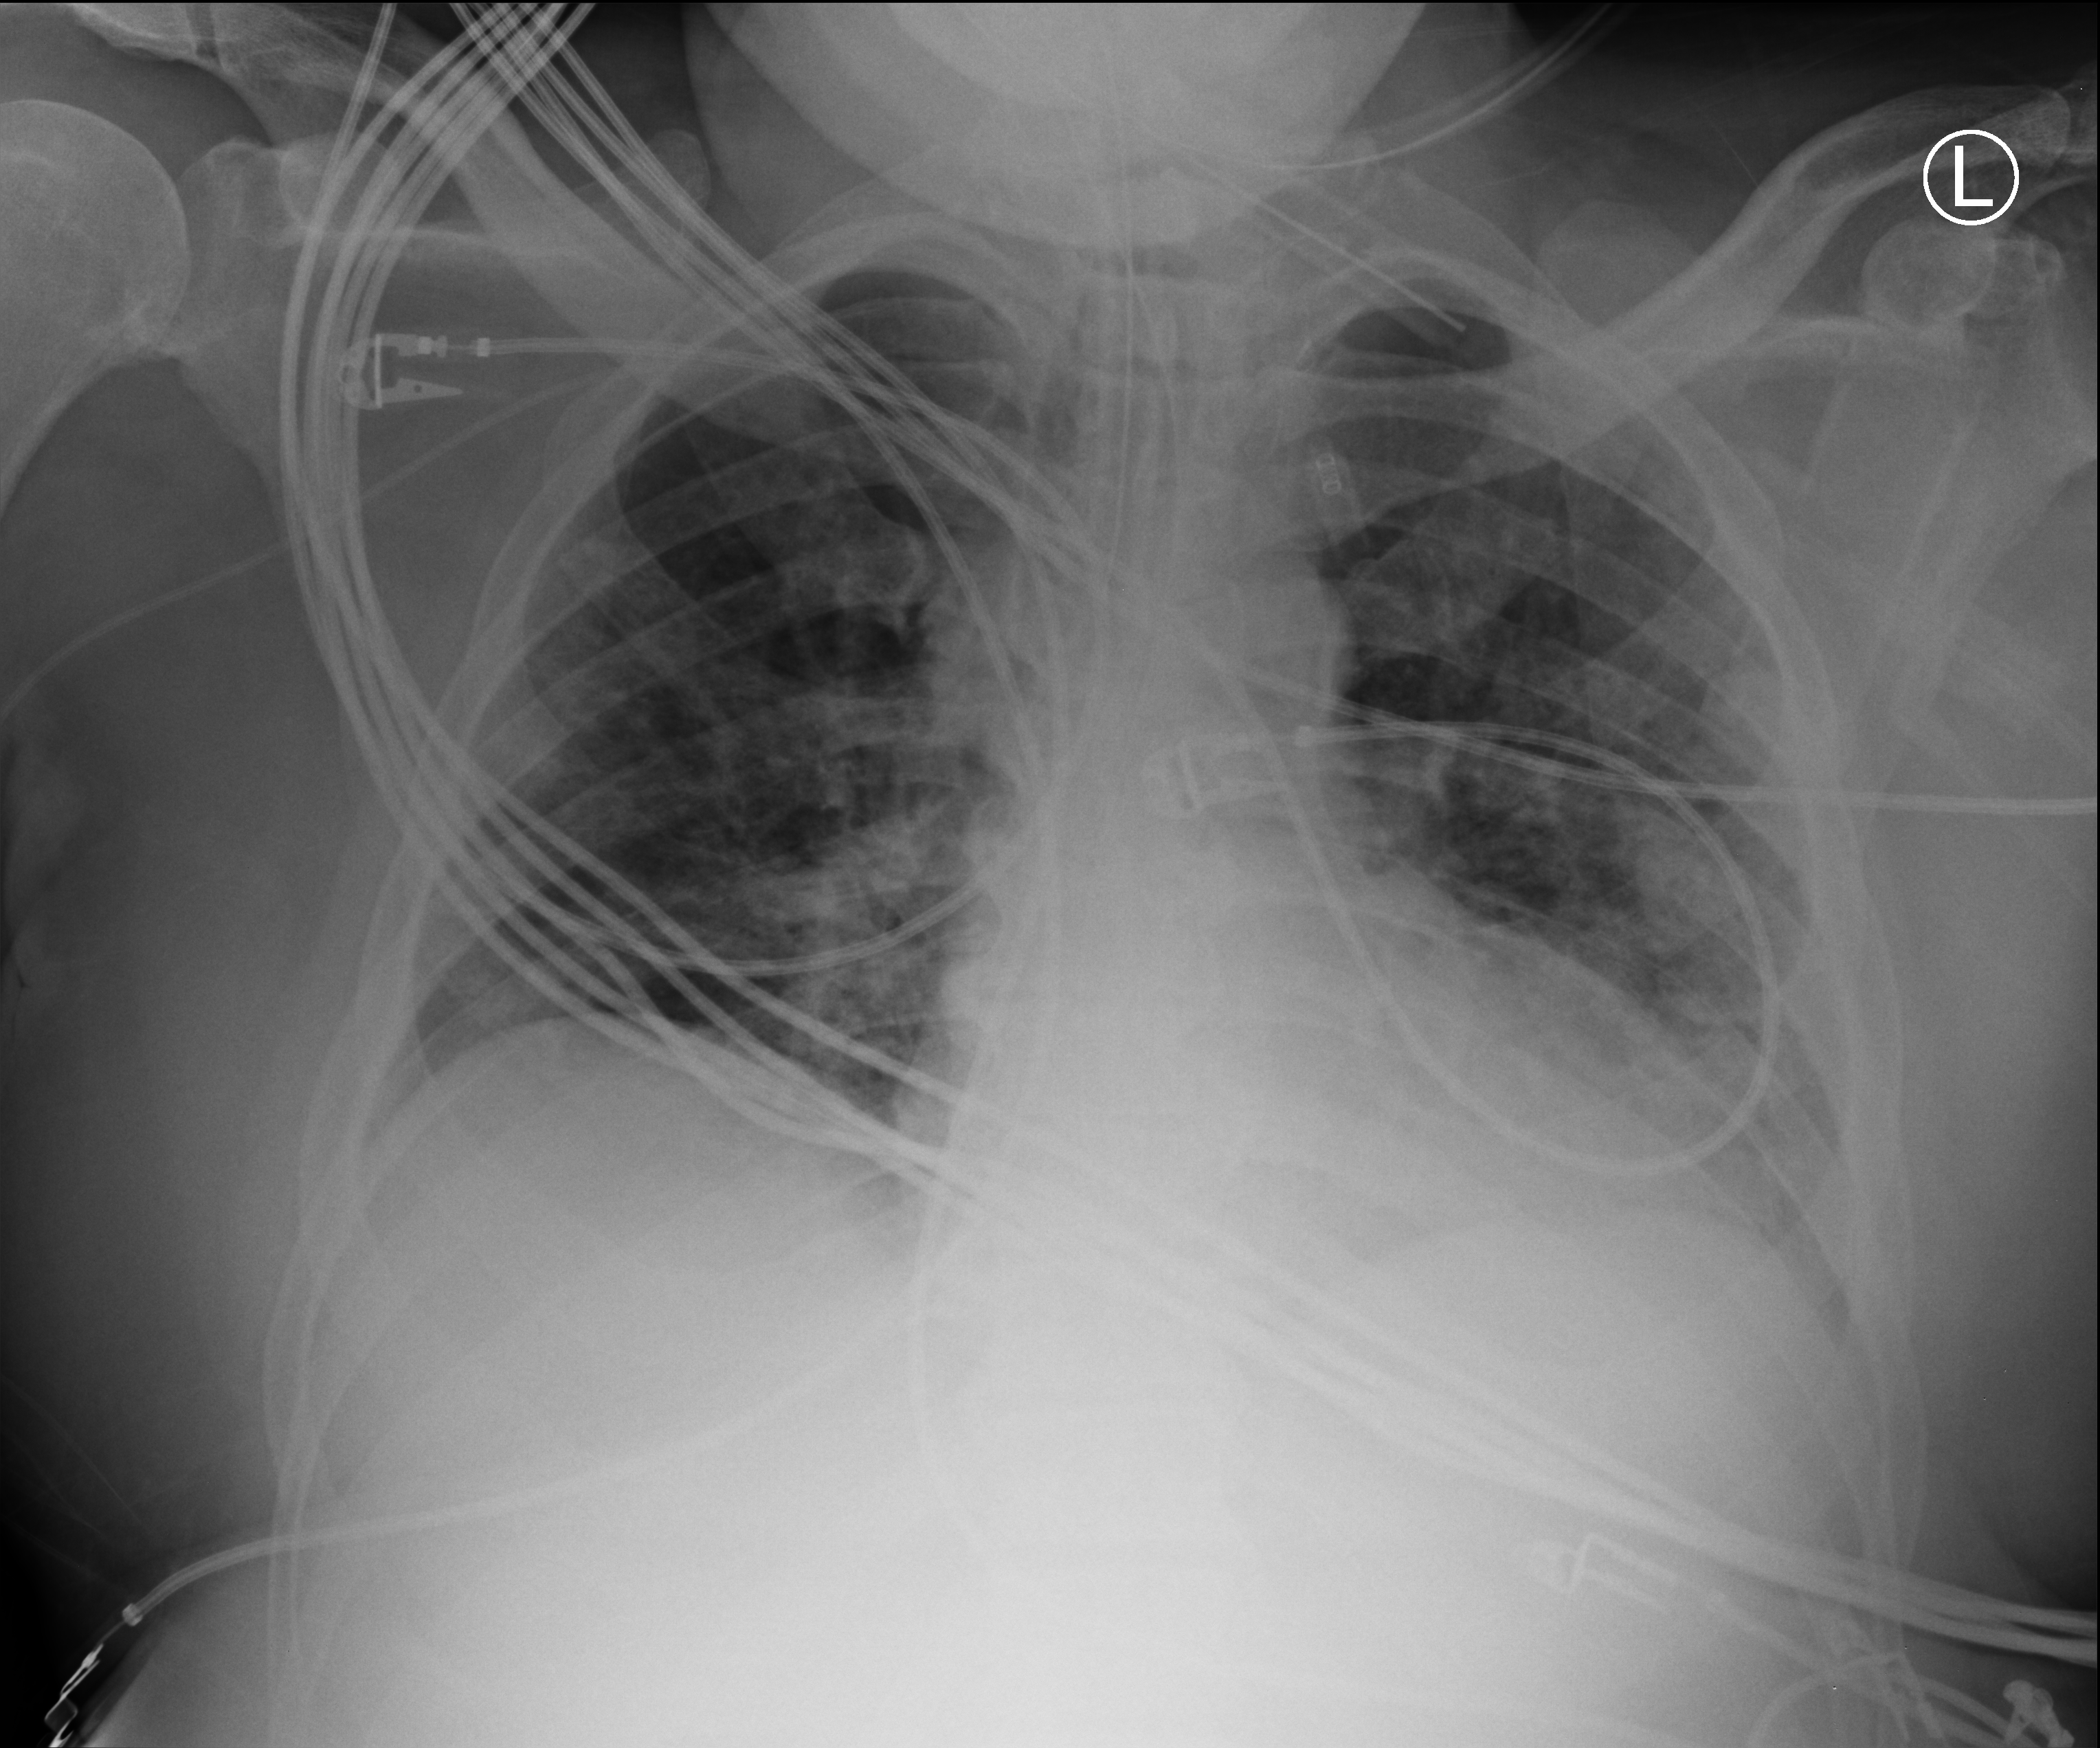
Portable chest radiograph, anteroposterior (AP) projection. Male patient hospitalised with COVID-19, age 18–59 years.
From the hospital-stay record, not from the radiograph (when in the stay this image was taken is not recorded): mechanically ventilated during this hospital stay: yes.